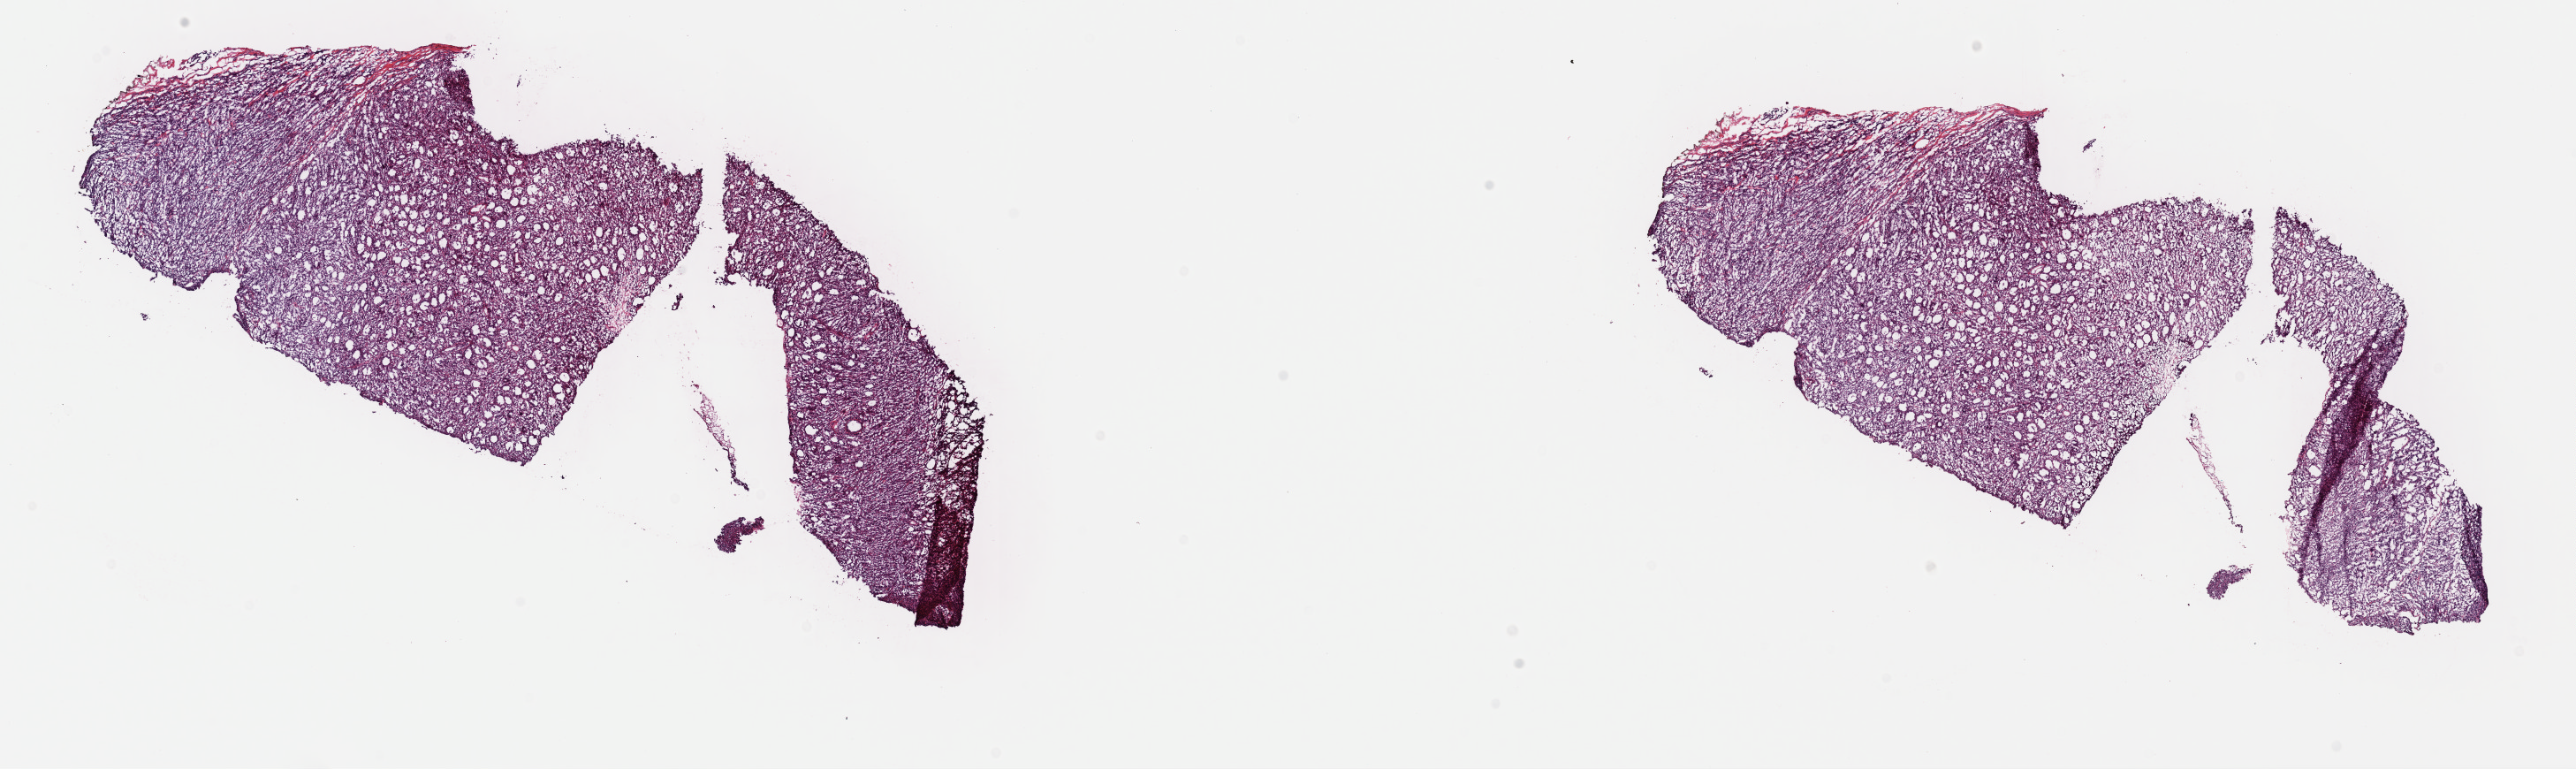
H&E-stained whole-slide image, low-resolution overview of the scanned area, about 23.0 x 6.9 mm (acquisition: 40x scan), frozen section from the top of the tissue portion, metastatic tumour sample. Patient: male, age at initial diagnosis 74 years. Composition of this section per pathologist review: tumour cells 85%, tumour nuclei 85%, normal cells 0%, stromal cells 15%, necrosis 0%. Inflammatory infiltration, as recorded: lymphocyte infiltration 0%, monocyte infiltration 0%, neutrophil infiltration 0%.
This section: metastatic tumour tissue. Patient diagnosis: Malignant melanoma, NOS.